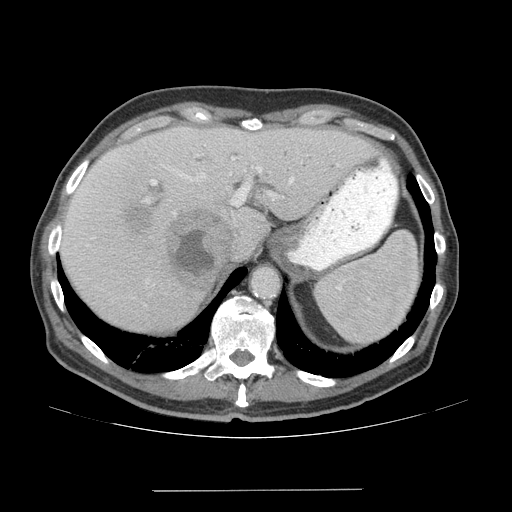
Contrast-enhanced abdominal CT (liver protocol), one axial slice; position 50 of 77 along the scan axis; 140 kVp; soft-tissue window (W 400 / L 40 HU); 2.5 mm slice thickness; 512 × 512 image matrix, field of view 400 × 400 mm. From the clinical record (not read from this slice): diagnosis: hepatocellular carcinoma (patient treated with transarterial chemoembolisation; whether this scan precedes or follows treatment is not stated here); TNM stage (as recorded): Stage-IVA; Child-Pugh class: A; tumour differentiation: well differentiated.
Structures marked on this image (semi-automatically segmented with operator editing):
- liver parenchyma outside the tumour (the mass and vessels are separate outlines, so this box may not span the whole liver): bounding box (x1, y1, x2, y2) in pixels: (60, 126, 376, 332)
- mass: (126, 205, 238, 292)
- liver vessels: (90, 153, 338, 214)